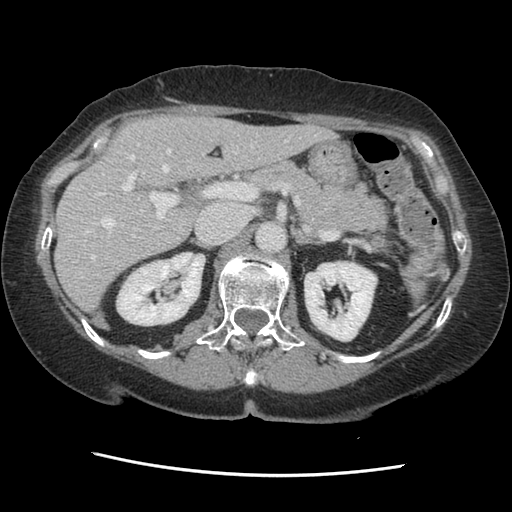
Contrast-enhanced abdominal CT, one axial slice. Position 83 of 141 along the scan axis. Soft-tissue window (W 400 / L 40 HU). 2.5 mm slice thickness. 512 × 512 image matrix. Female patient, age 61 years. Case-level facts recorded for this patient, not image findings: diagnosis: colorectal cancer liver metastases, imaged before liver resection; multiple liver metastases: no; largest metastasis: 2.4 cm; disease in both lobes: no.
Outlined on this slice (manually delineated by an expert):
- hepatic veins: bounding box [x1, y1, x2, y2] px = [91, 140, 287, 260]
- liver: [56, 116, 328, 310]
- planned liver remnant (the part of the liver to remain after resection): [56, 116, 328, 310]
- portal vein (with intrahepatic branches): [96, 155, 257, 227]